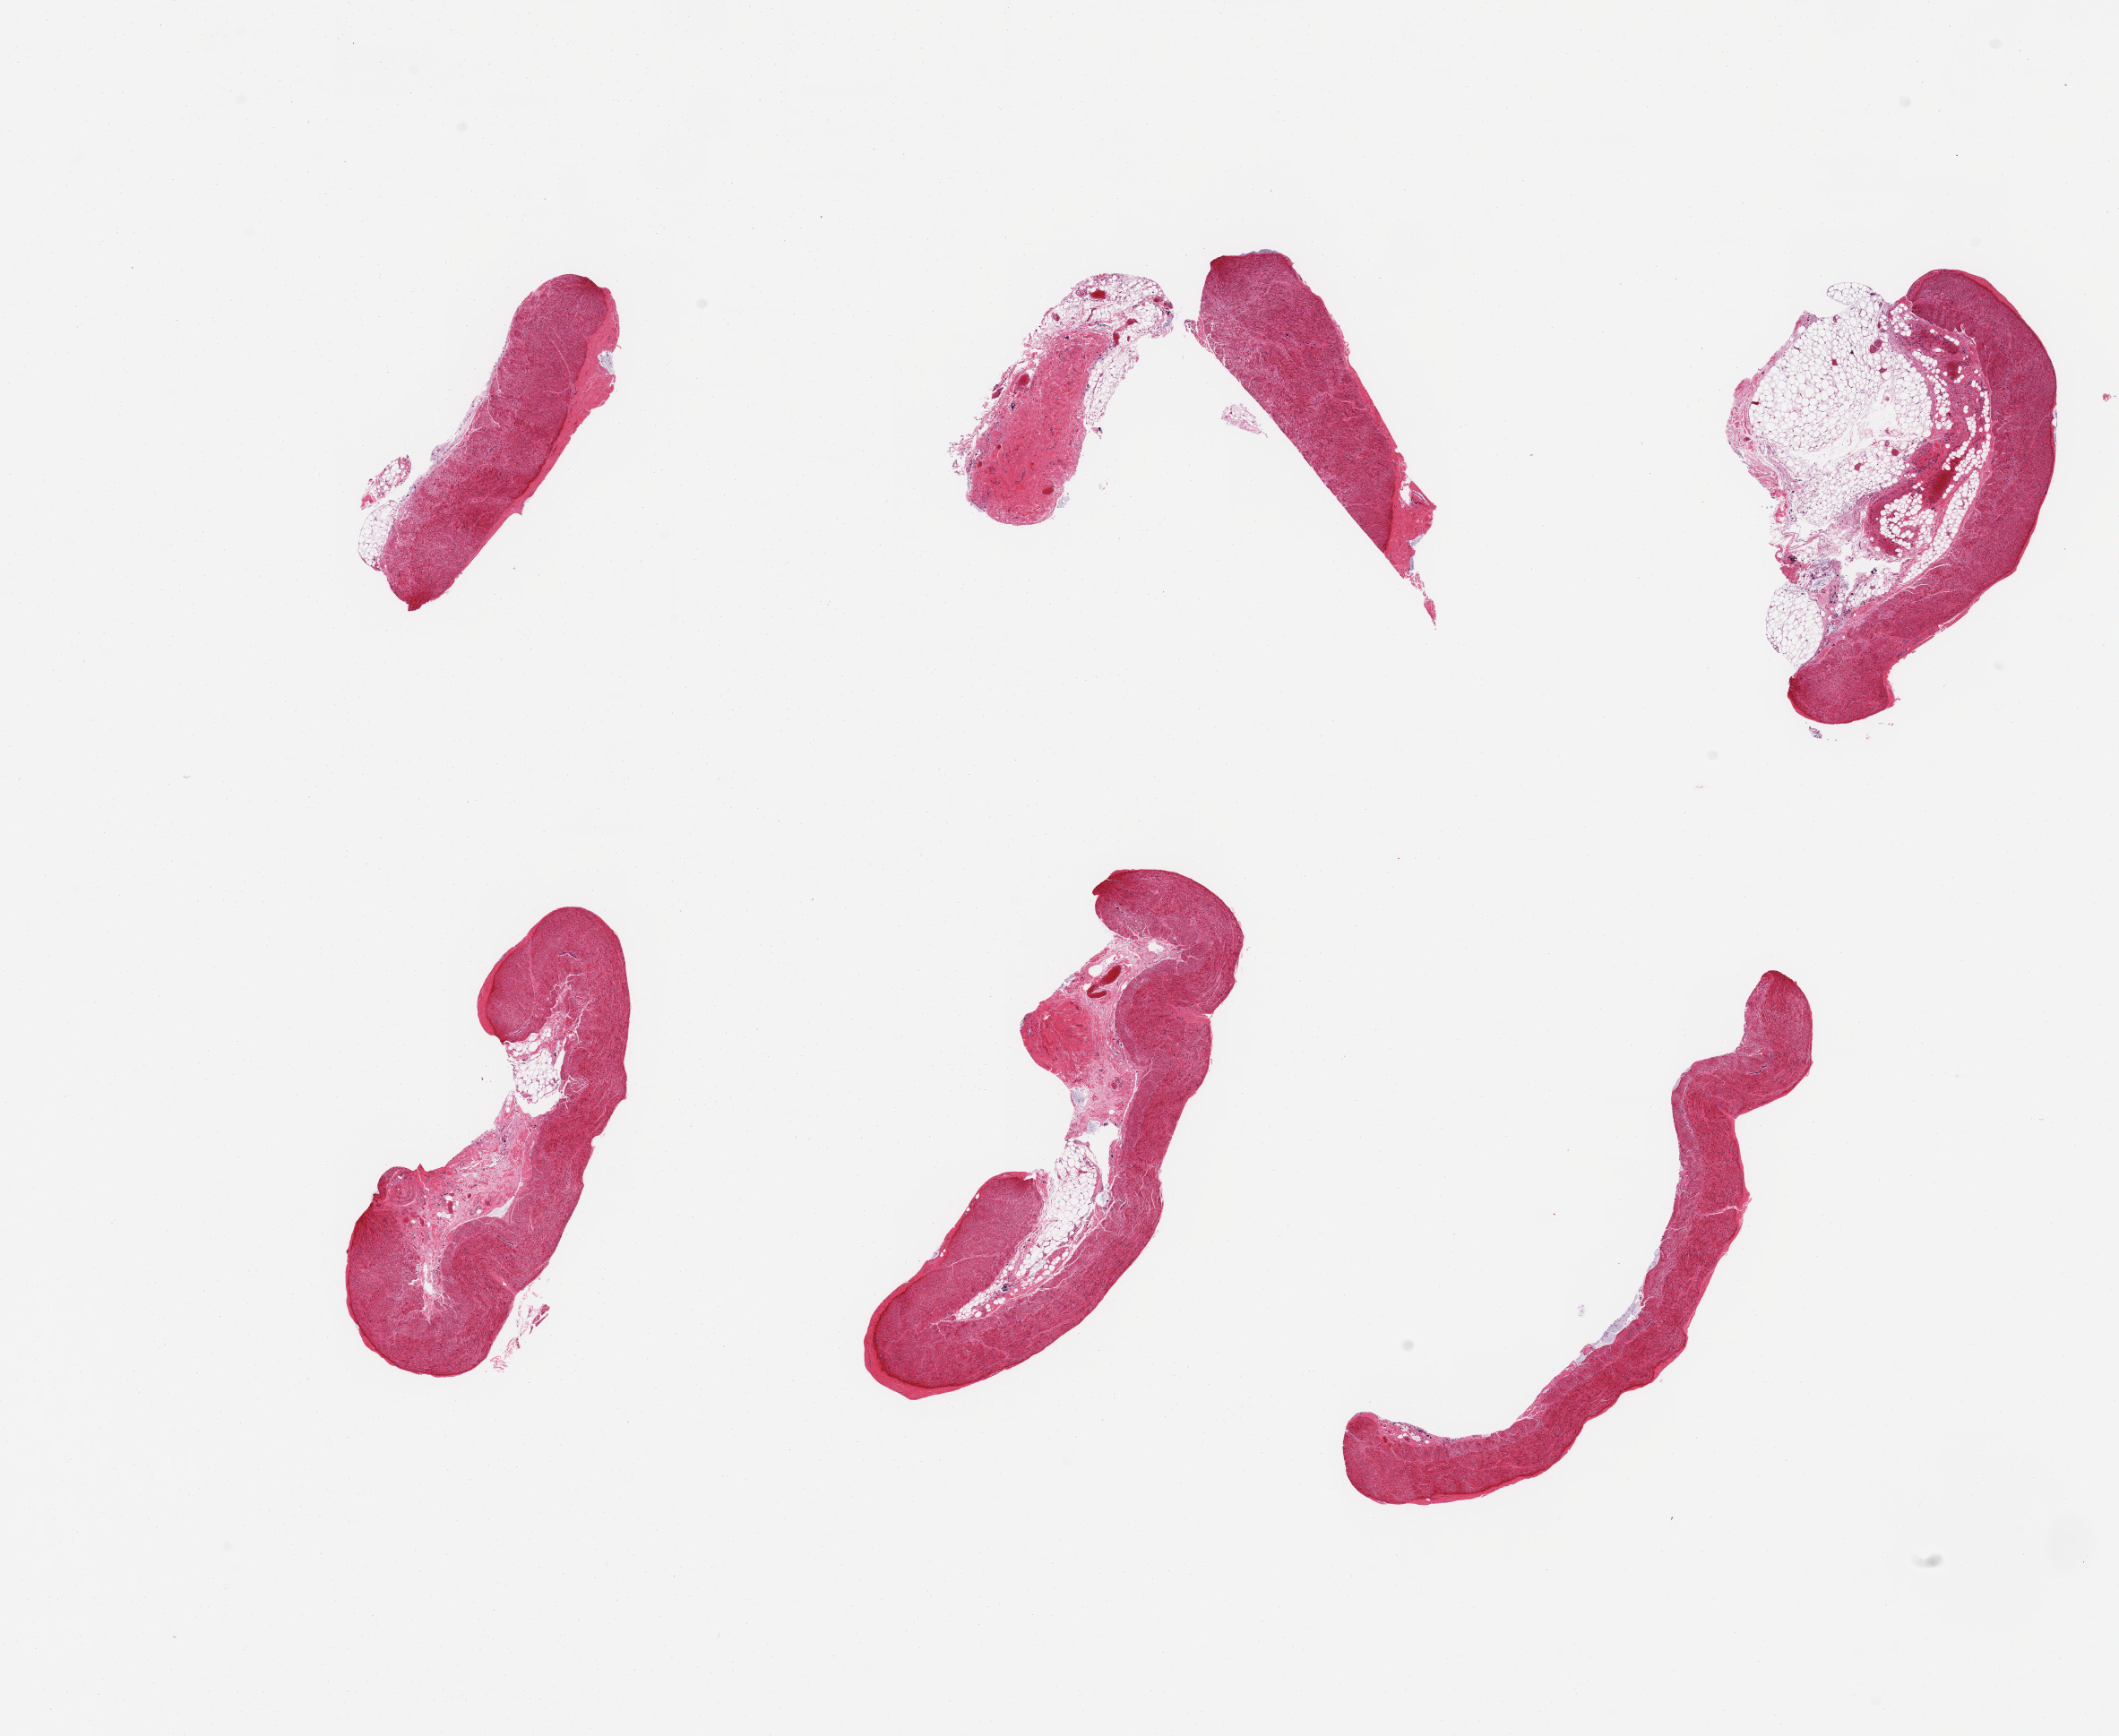
Digitized hematoxylin and eosin (H&E)-stained section, brightfield, whole scanned area (about 18.7 x 15.3 mm) shown as a low-resolution overview. PAXgene-fixed, paraffin-embedded tissue. Section of sigmoid colon (target tissue). Donor tissue sample.
Reviewer comment on this tissue sample: 6 pieces; extraneous fibrous and fatty tissue in several pieces.